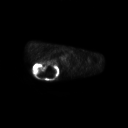
FDG PET of an extremity soft-tissue mass (from a PET/CT study), one axial slice; slice 204 of 267 in the series (ordered by position); 128 × 128 image matrix, field of view 700 × 700 mm. Male patient, age 61 years. From the clinical record (not read from this slice): histological type: pleiomorphic spindle cell undifferentiated; grade: high; site of the primary tumour: right parascapusular.
Annotated regions visible in this slice (expert contour drawn on MRI and transferred to this co-registered scan by the dataset authors):
- gross tumour volume including surrounding oedema: box from (x=32, y=61) to (x=61, y=78) px
- gross tumour volume (mass): (x=33, y=62)–(x=58, y=77)